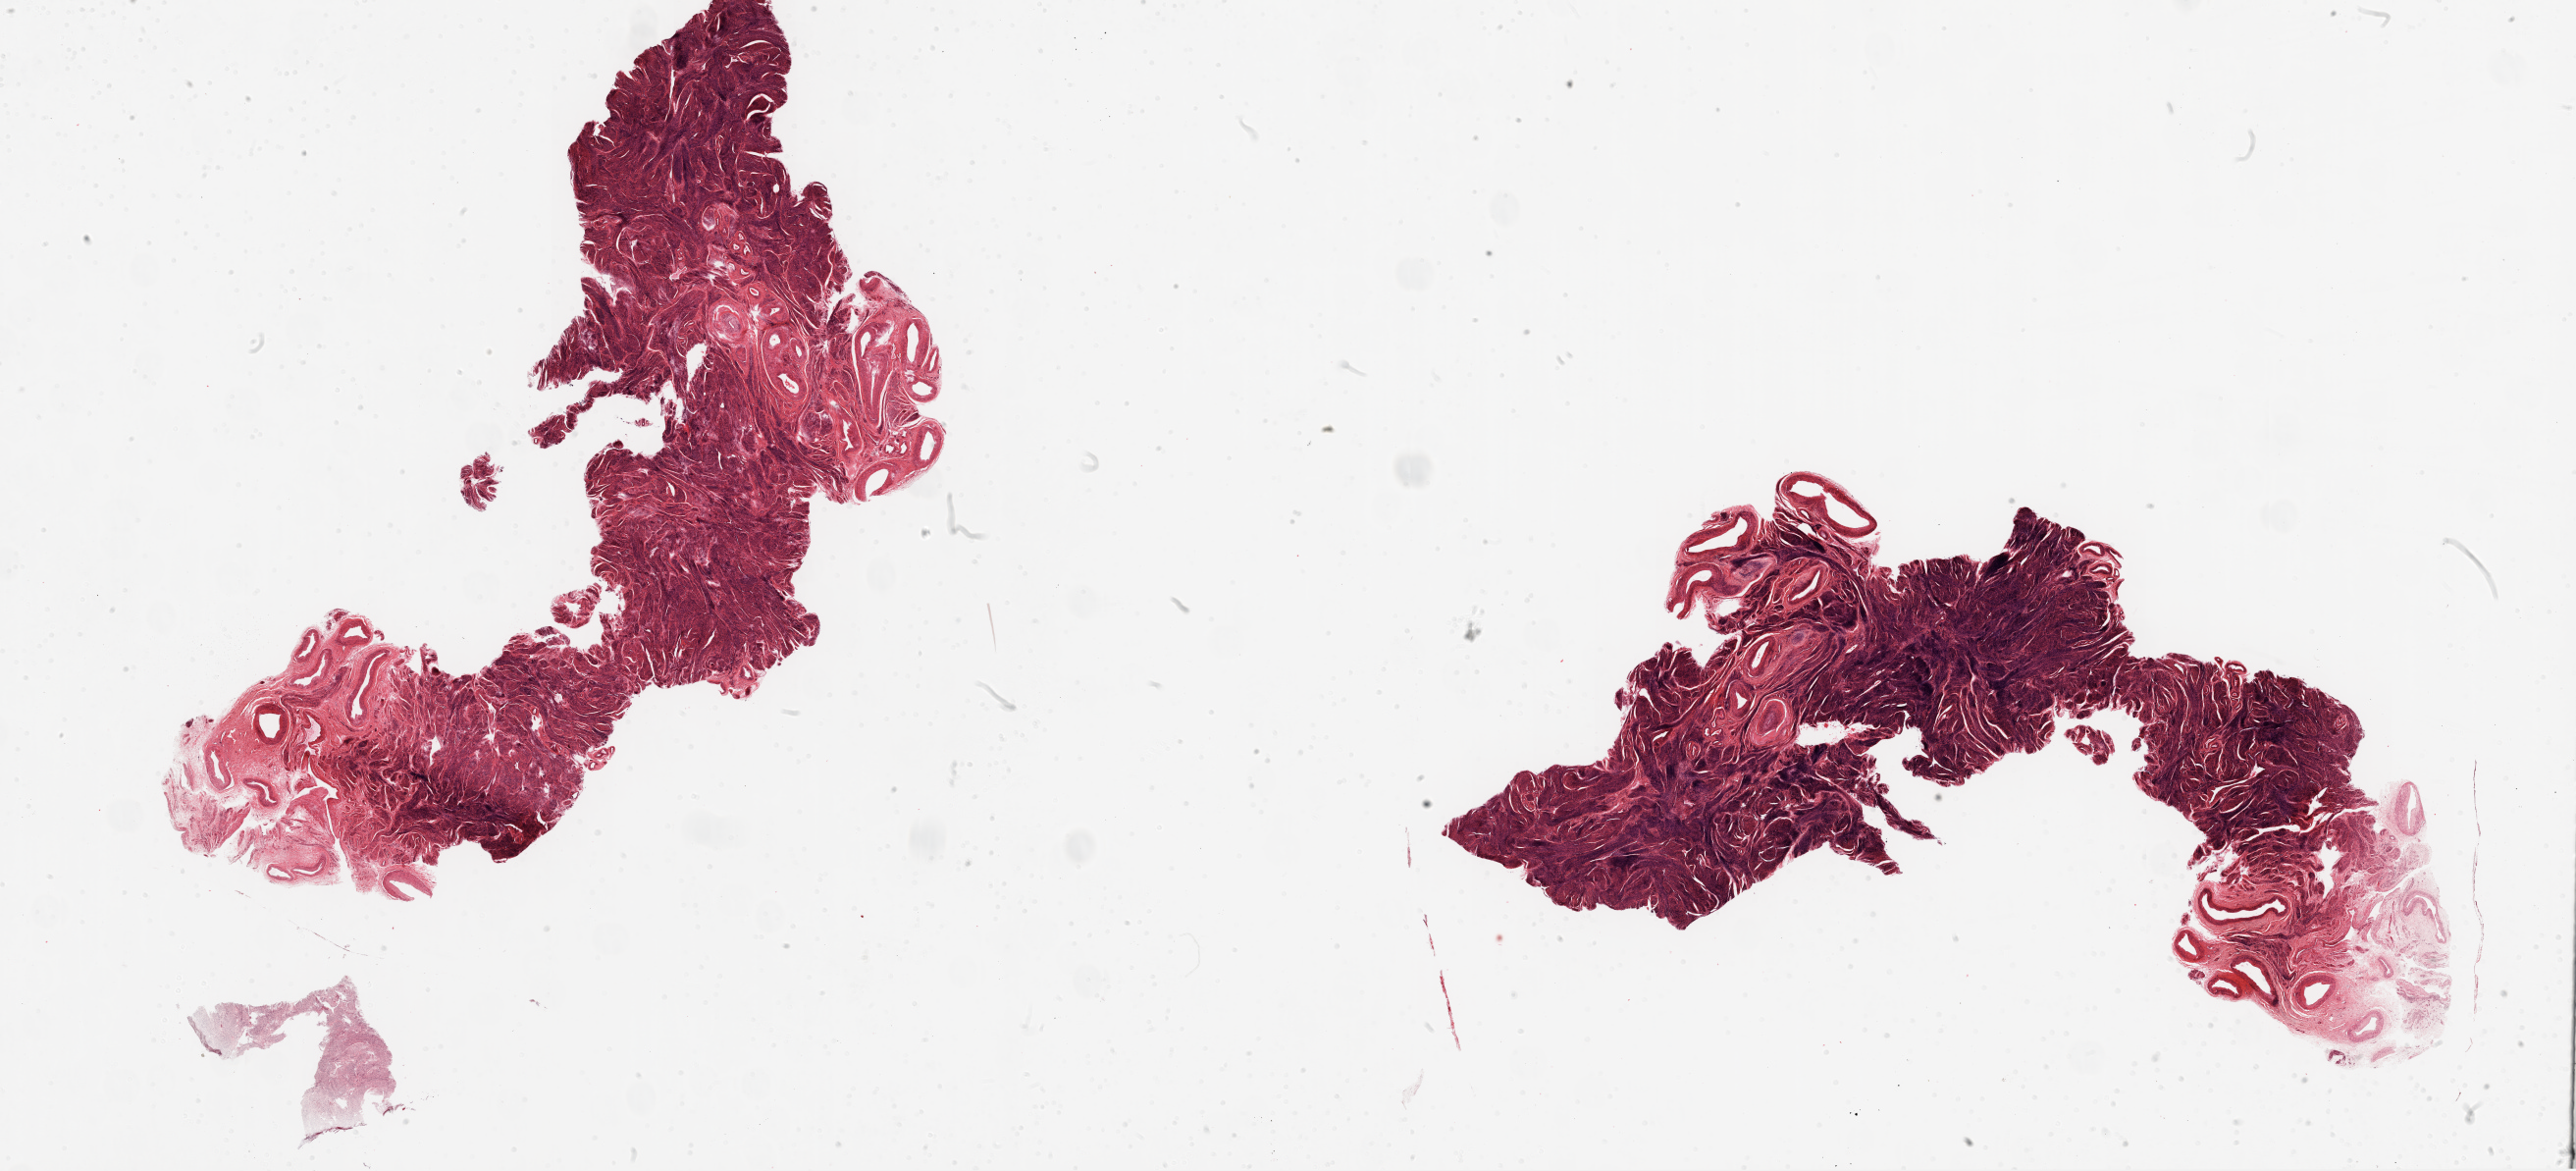
Digitized H&E-stained tissue section (whole slide) — a low-resolution overview of the entire scanned area, about 42.1 x 19.1 mm (from a 20x scan). Frozen section from the top of the tissue portion. Sample: solid tissue normal (non-tumour tissue), ovary. Female, age 69 years at initial diagnosis.
This section: solid tissue normal sample (biorepository sample class). Patient diagnosis: Serous cystadenocarcinoma, NOS.